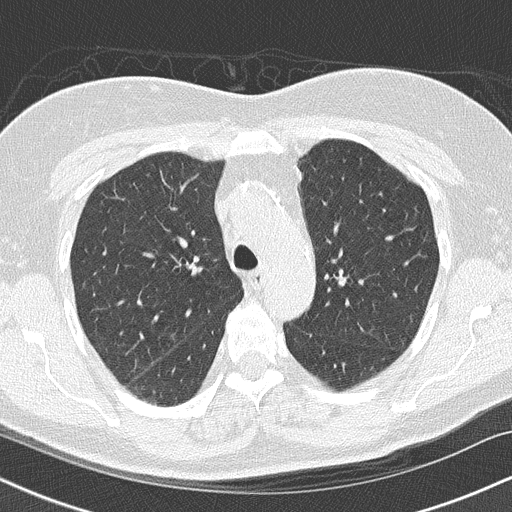
Chest CT (low-dose screening protocol), one axial image; first (baseline) screen; lung window (W 1500 / L -600 HU); lung (sharp) reconstruction kernel (B50f); 512 × 512 image matrix, field of view 320 × 320 mm. Female participant, aged 66 years at enrolment.
- Lesion marked by an expert reader, bounding box (x1, y1, x2, y2) in pixels: (158, 325, 188, 350).
- Screening reader's record for this exam (one nodule recorded; not confirmed to be the boxed lesion): non-calcified nodule or mass ≥4 mm, right lower lobe, 10 × 8 mm, smooth margins, soft tissue attenuation.
- Participant outcome: lung cancer diagnosed 96 days after this screen — squamous cell carcinoma, keratinizing, NOS, right upper lobe, right middle lobe, poorly differentiated (G3), stage IA (AJCC 6th edition), 14 mm at pathology.